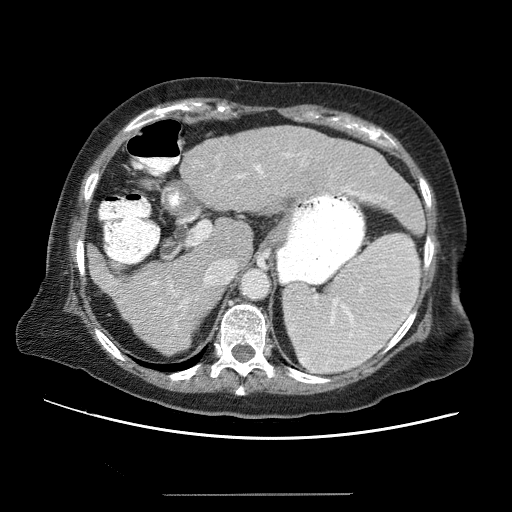
Contrast-enhanced abdominal CT (liver protocol), one axial slice; position 39 of 65 along the scan axis; 120 kVp; soft-tissue window (W 400 / L 40 HU); 512 × 512 image matrix. From the clinical record (not read from this slice): diagnosis: hepatocellular carcinoma (patient treated with transarterial chemoembolisation; whether this scan precedes or follows treatment is not stated here); TNM stage (as recorded): Stage-IIIB; Child-Pugh class: A.
Annotated regions visible in this slice (semi-automatic segmentation, software-assisted and operator-edited):
- liver parenchyma outside the tumour (the mass and vessels are separate outlines, so this box may not span the whole liver): box from (x=86, y=126) to (x=416, y=354) px
- liver vessels: (x=108, y=132)–(x=403, y=323)